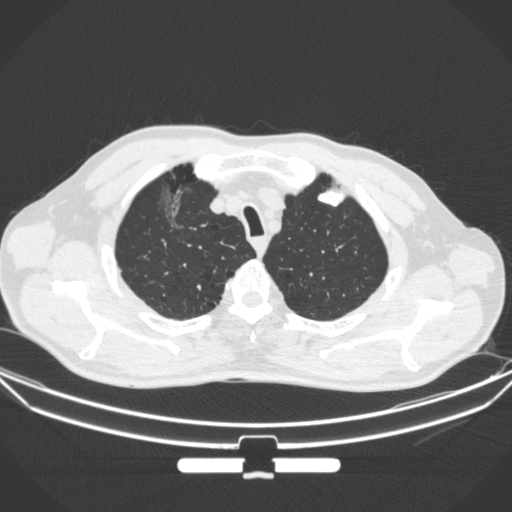
Chest CT, one axial slice; position 293 of 355 along the scan axis; lung window (W 1500 / L -600 HU); 512 × 512 image matrix, field of view 399 × 399 mm. Patient: male, 67 years. Case-level facts recorded for this patient, not image findings: clinical TNM (as recorded): T1c N0 M0.
Structures marked on this image (rectangle marked by the reading radiologist):
- lung tumour (recorded histology: adenocarcinoma): box from (x=155, y=178) to (x=207, y=245) px